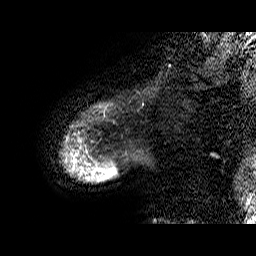
Breast MRI (dynamic contrast-enhanced), one sagittal slice. Slice 1 of 60 in the series (ordered by position). Dynamic contrast-enhanced series, time point 2 of 6 at this slice position (early post-contrast). 1.5 T. TE 6.4 ms, TR 32.9 ms. 4 mm slice thickness. 256 × 256 image matrix, field of view 200 × 200 mm. Female patient. Case-level facts recorded for this patient, not image findings: setting: breast cancer imaged before/during neoadjuvant chemotherapy; receptor status: HR-positive, HER2-negative.
Annotated regions visible in this slice (semi-automatic segmentation, software-assisted and operator-edited):
- analysis volume of interest (the breast-tissue region the enhancement analysis was run in; not a lesion): bounding box (x1, y1, x2, y2) in pixels: (61, 101, 127, 183)
- tumour enhancement mask (voxels above the 100 % enhancement threshold inside the analysis volume of interest): (65, 154, 98, 170)